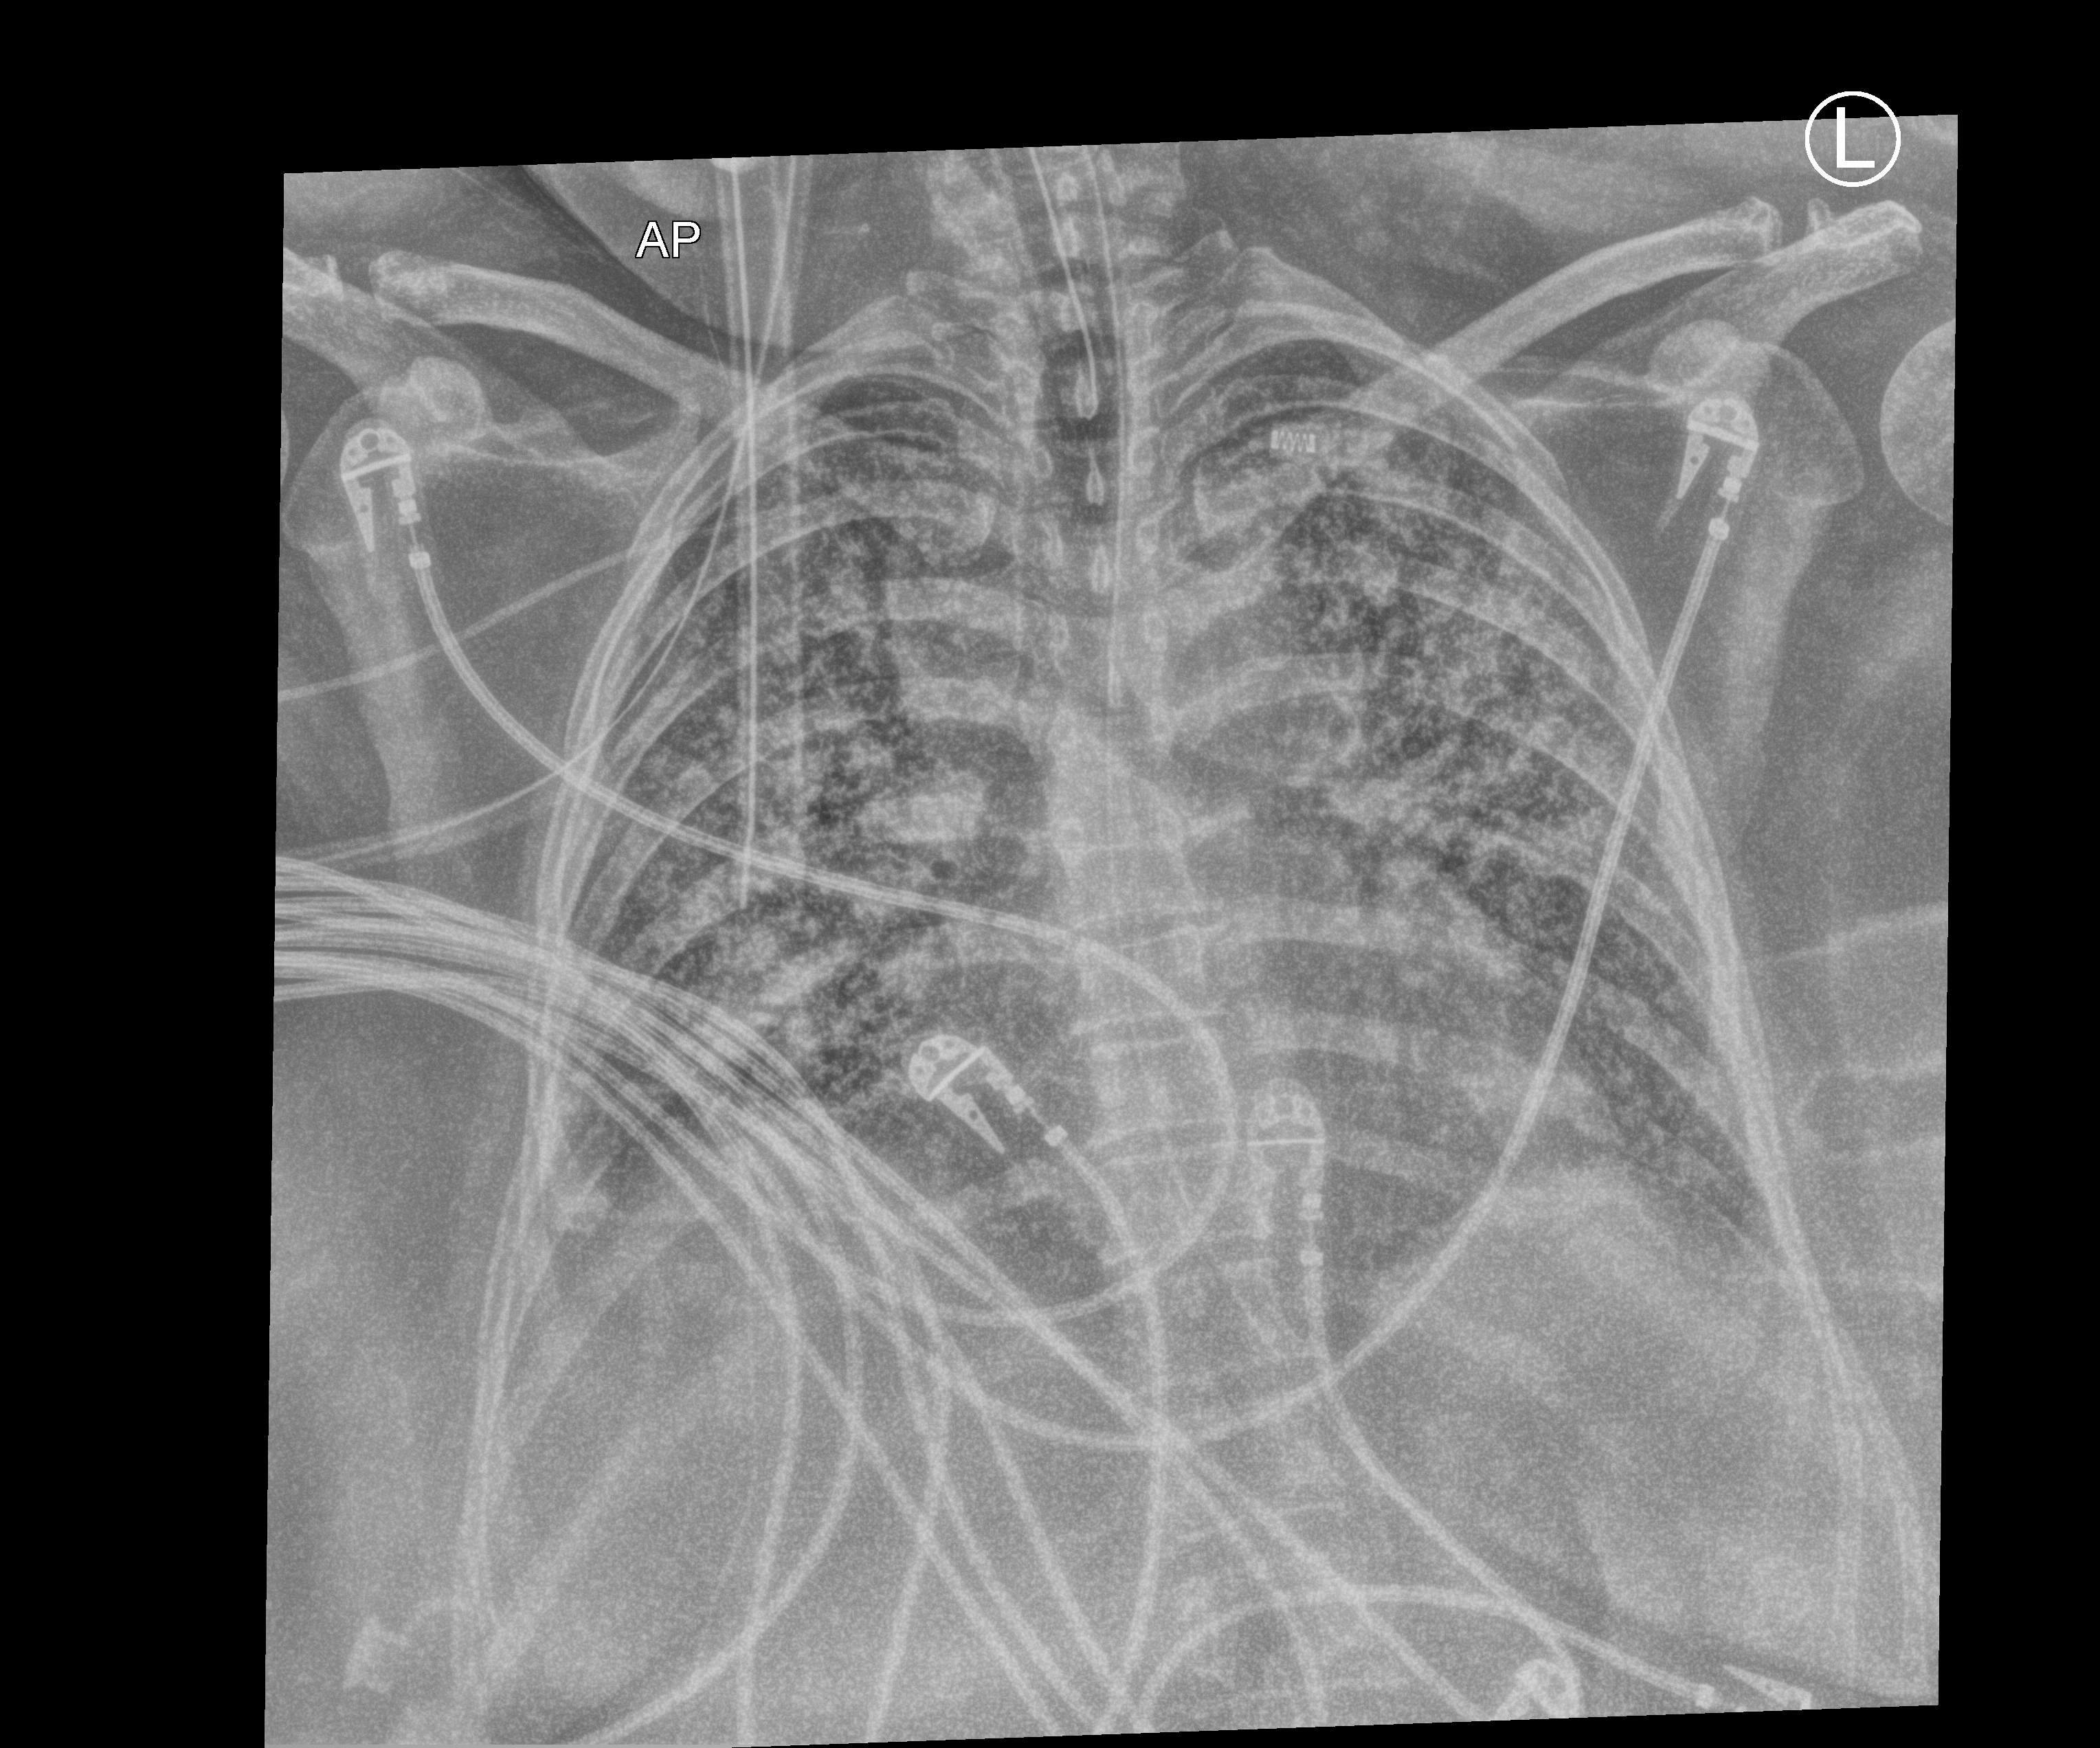
Chest X-ray (portable), anteroposterior (AP) projection. Female patient hospitalised with COVID-19, age 18–59 years.
Admission-level facts for this patient (not findings on this image; timing relative to this image not recorded):
- admitted to intensive care during this hospital stay: yes